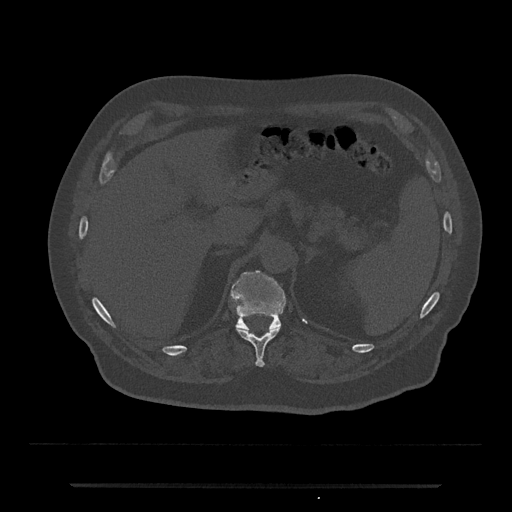
CT including the spine, one axial slice; 120 kVp; bone window (W 1800 / L 400 HU); 0.5 mm slice thickness; 512 × 512 image matrix, field of view 434 × 434 mm. Male patient, age 80 years. From the clinical record (not read from this slice): primary cancer: prostate.
Outlined on this slice (semi-automatically segmented with operator editing):
- T11 vertebra: bounding box [x1, y1, x2, y2] px = [237, 328, 280, 367]
- T12 vertebra: [231, 270, 286, 331]